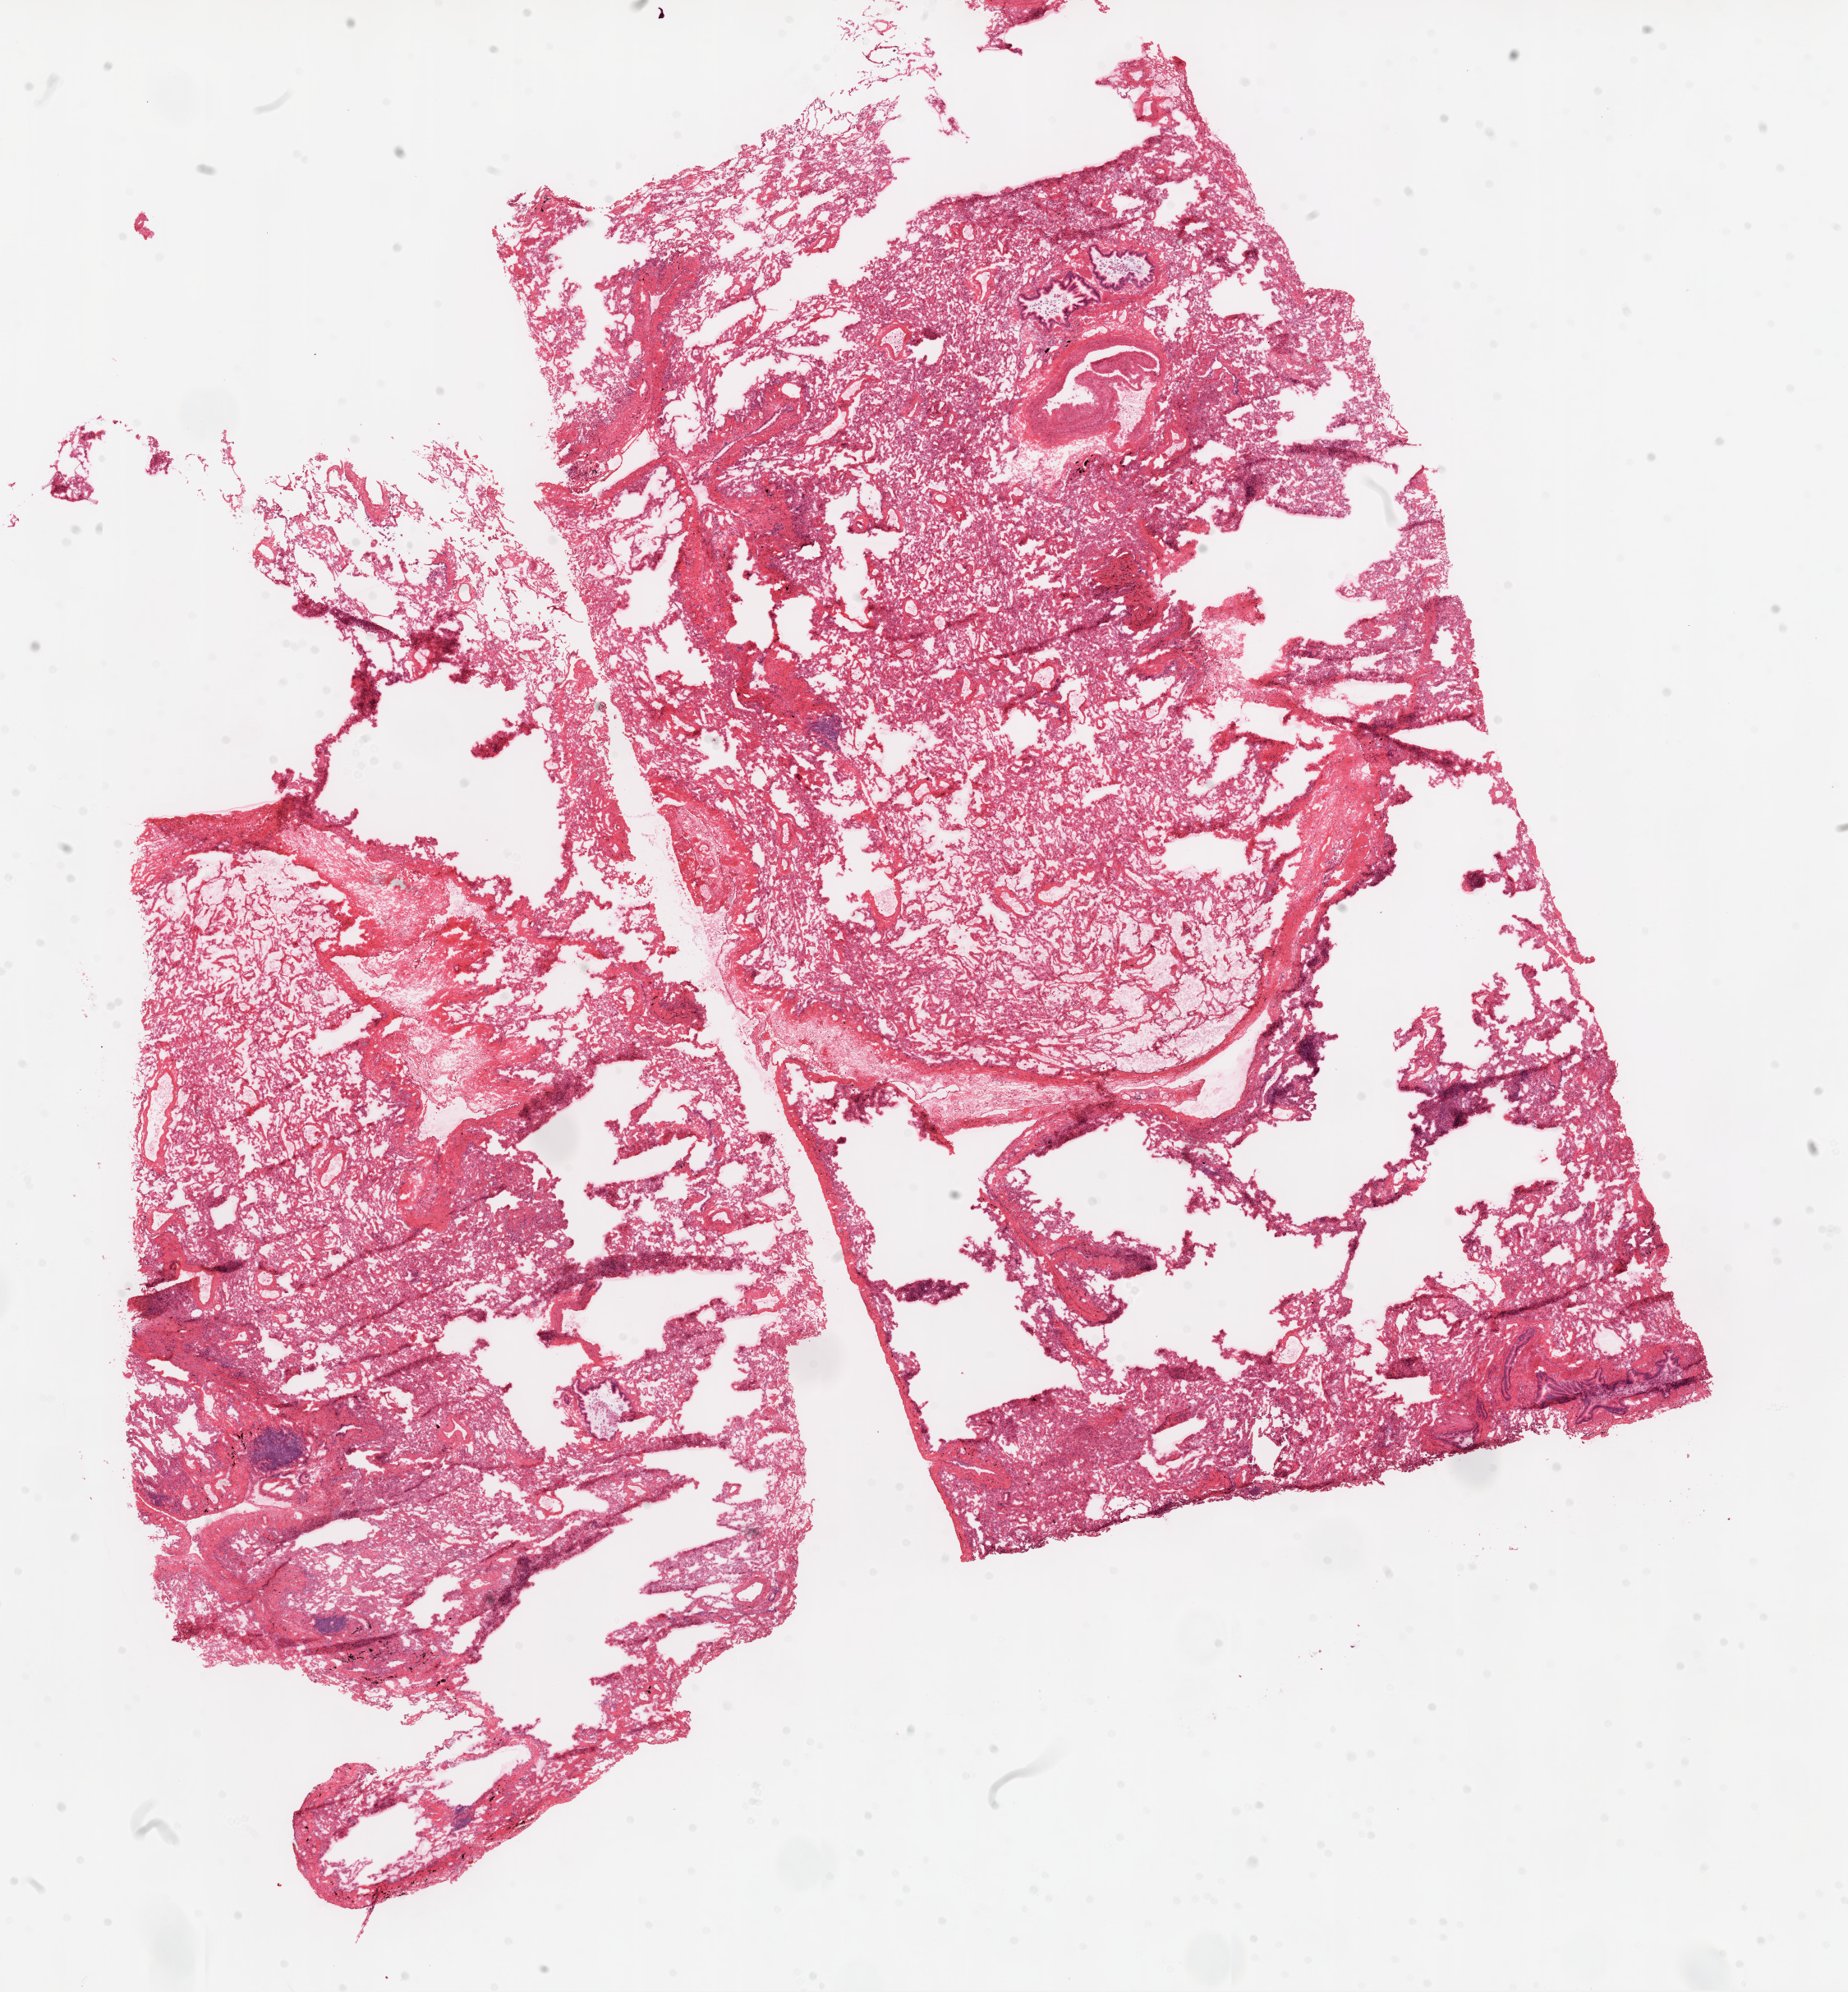
H&E whole-slide image, whole scanned area (about 18.1 x 19.5 mm, from a 20x scan) shown as a low-resolution overview. Frozen section from the top of the tissue portion. Lung, solid tissue normal (non-tumour tissue) sample. Female patient; age at initial diagnosis 76 years.
This section: solid tissue normal (non-tumour) sample from the same patient. Patient diagnosis: Squamous cell carcinoma, NOS (upper lobe, lung).